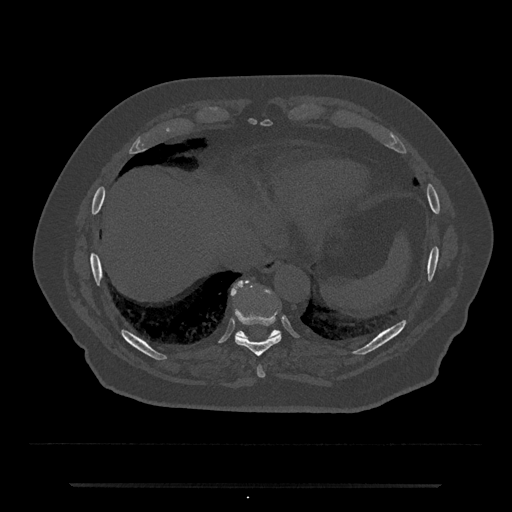
CT including the spine, one axial slice. Position 744 of 797 along the scan axis. Reconstruction kernel Br40s/3. 120 kVp. Bone window (W 1800 / L 400 HU). 0.5 mm slice thickness. 512 × 512 image matrix, field of view 434 × 434 mm. Patient: male, 80 years. From the clinical record (not read from this slice): primary cancer: prostate; vertebrae with lytic lesions (as recorded): L1, T11.
Annotated regions visible in this slice (semi-automatic segmentation, software-assisted and operator-edited):
- T10 vertebra: bounding box <231,281,281,339> (left, top, right, bottom; pixels)
- T8 vertebra: <257,366,265,378>
- T9 vertebra: <235,315,281,357>